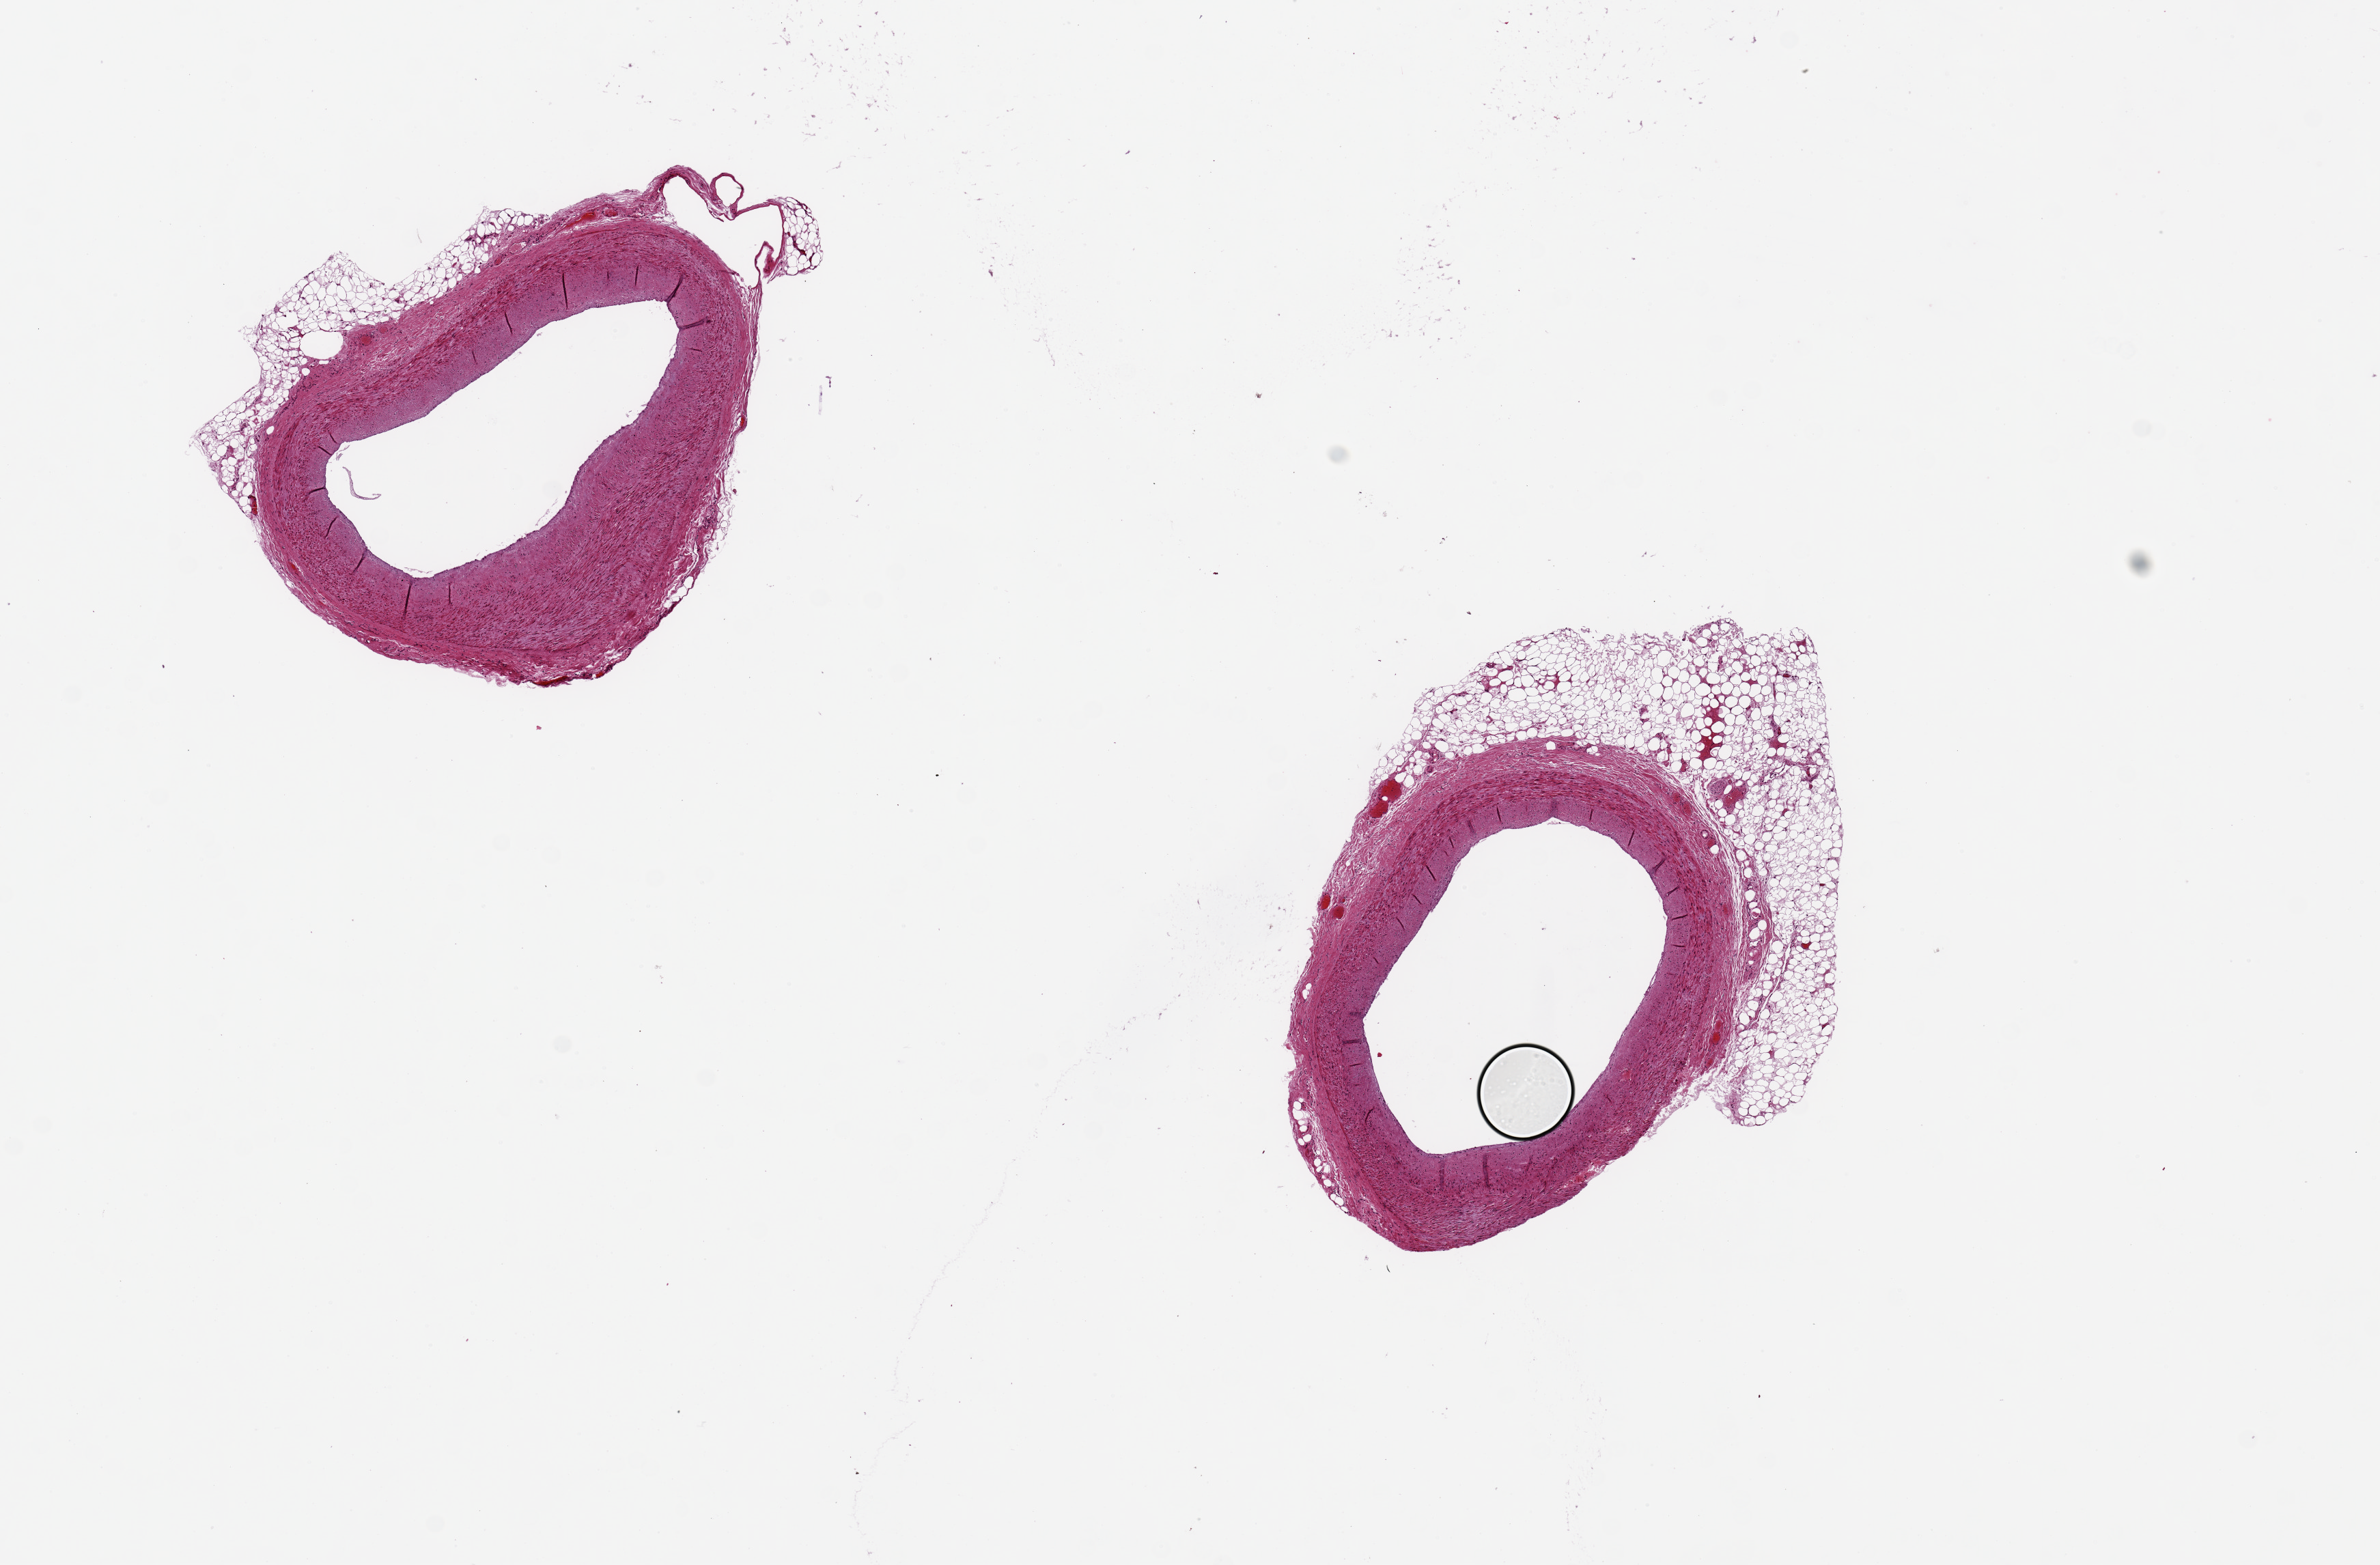
Hematoxylin and eosin (H&E) whole-slide image, a low-resolution overview of the entire scanned area, about 13.8 x 9.1 mm, PAXgene-fixed, paraffin-embedded tissue, sampled site (target tissue): coronary artery, tissue donor sample.
Reviewer comment on this tissue sample: 2 pieces ~2.5mm d; Both with adherent partly encasing fat, up to ~1mm thick.